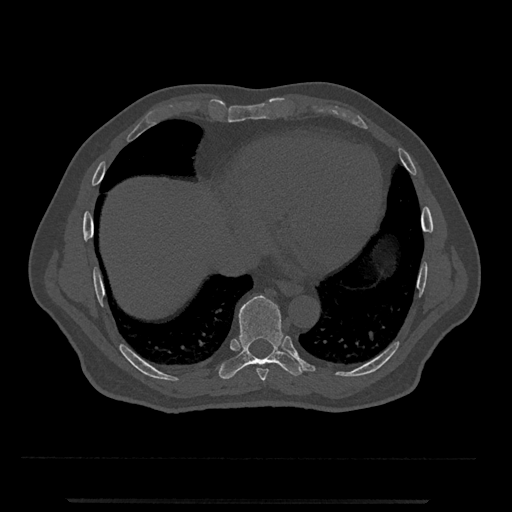
CT including the spine, one axial slice; slice 588 of 797 in the series (ordered by position); reconstruction kernel Br40s/3; bone window (W 1800 / L 400 HU); 512 × 512 image matrix, field of view 419 × 419 mm. Patient: male, 63 years. From the clinical record (not read from this slice): primary cancer: prostate.
Outlined on this slice (semi-automatically segmented with operator editing):
- T8 vertebra: box from (x=257, y=368) to (x=269, y=381) px
- T9 vertebra: (x=219, y=295)–(x=304, y=379)